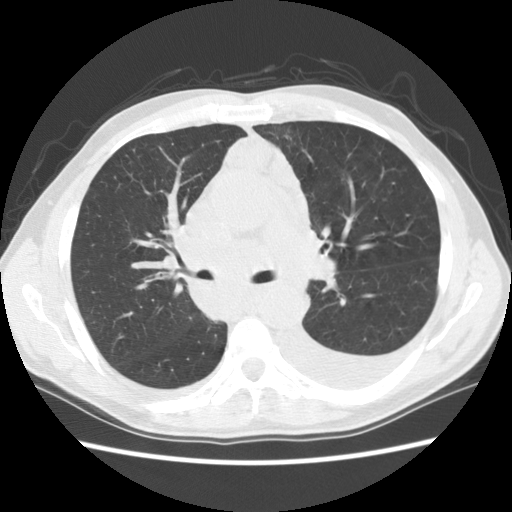
Chest CT (low-dose screening protocol), one axial image; baseline annual screen; lung window (W 1500 / L -600 HU); 2.5 mm slice thickness; standard (soft-tissue) reconstruction kernel (STANDARD); 512 × 512 image matrix. Male participant, aged 60 years at enrolment.
Expert reader's lesion annotation, bounding box <178,237,294,327> (left, top, right, bottom; pixels). Screening reader's record for this exam: no non-calcified nodule ≥4 mm recorded. Official screen result: negative screen, significant abnormalities not suspicious for lung cancer.